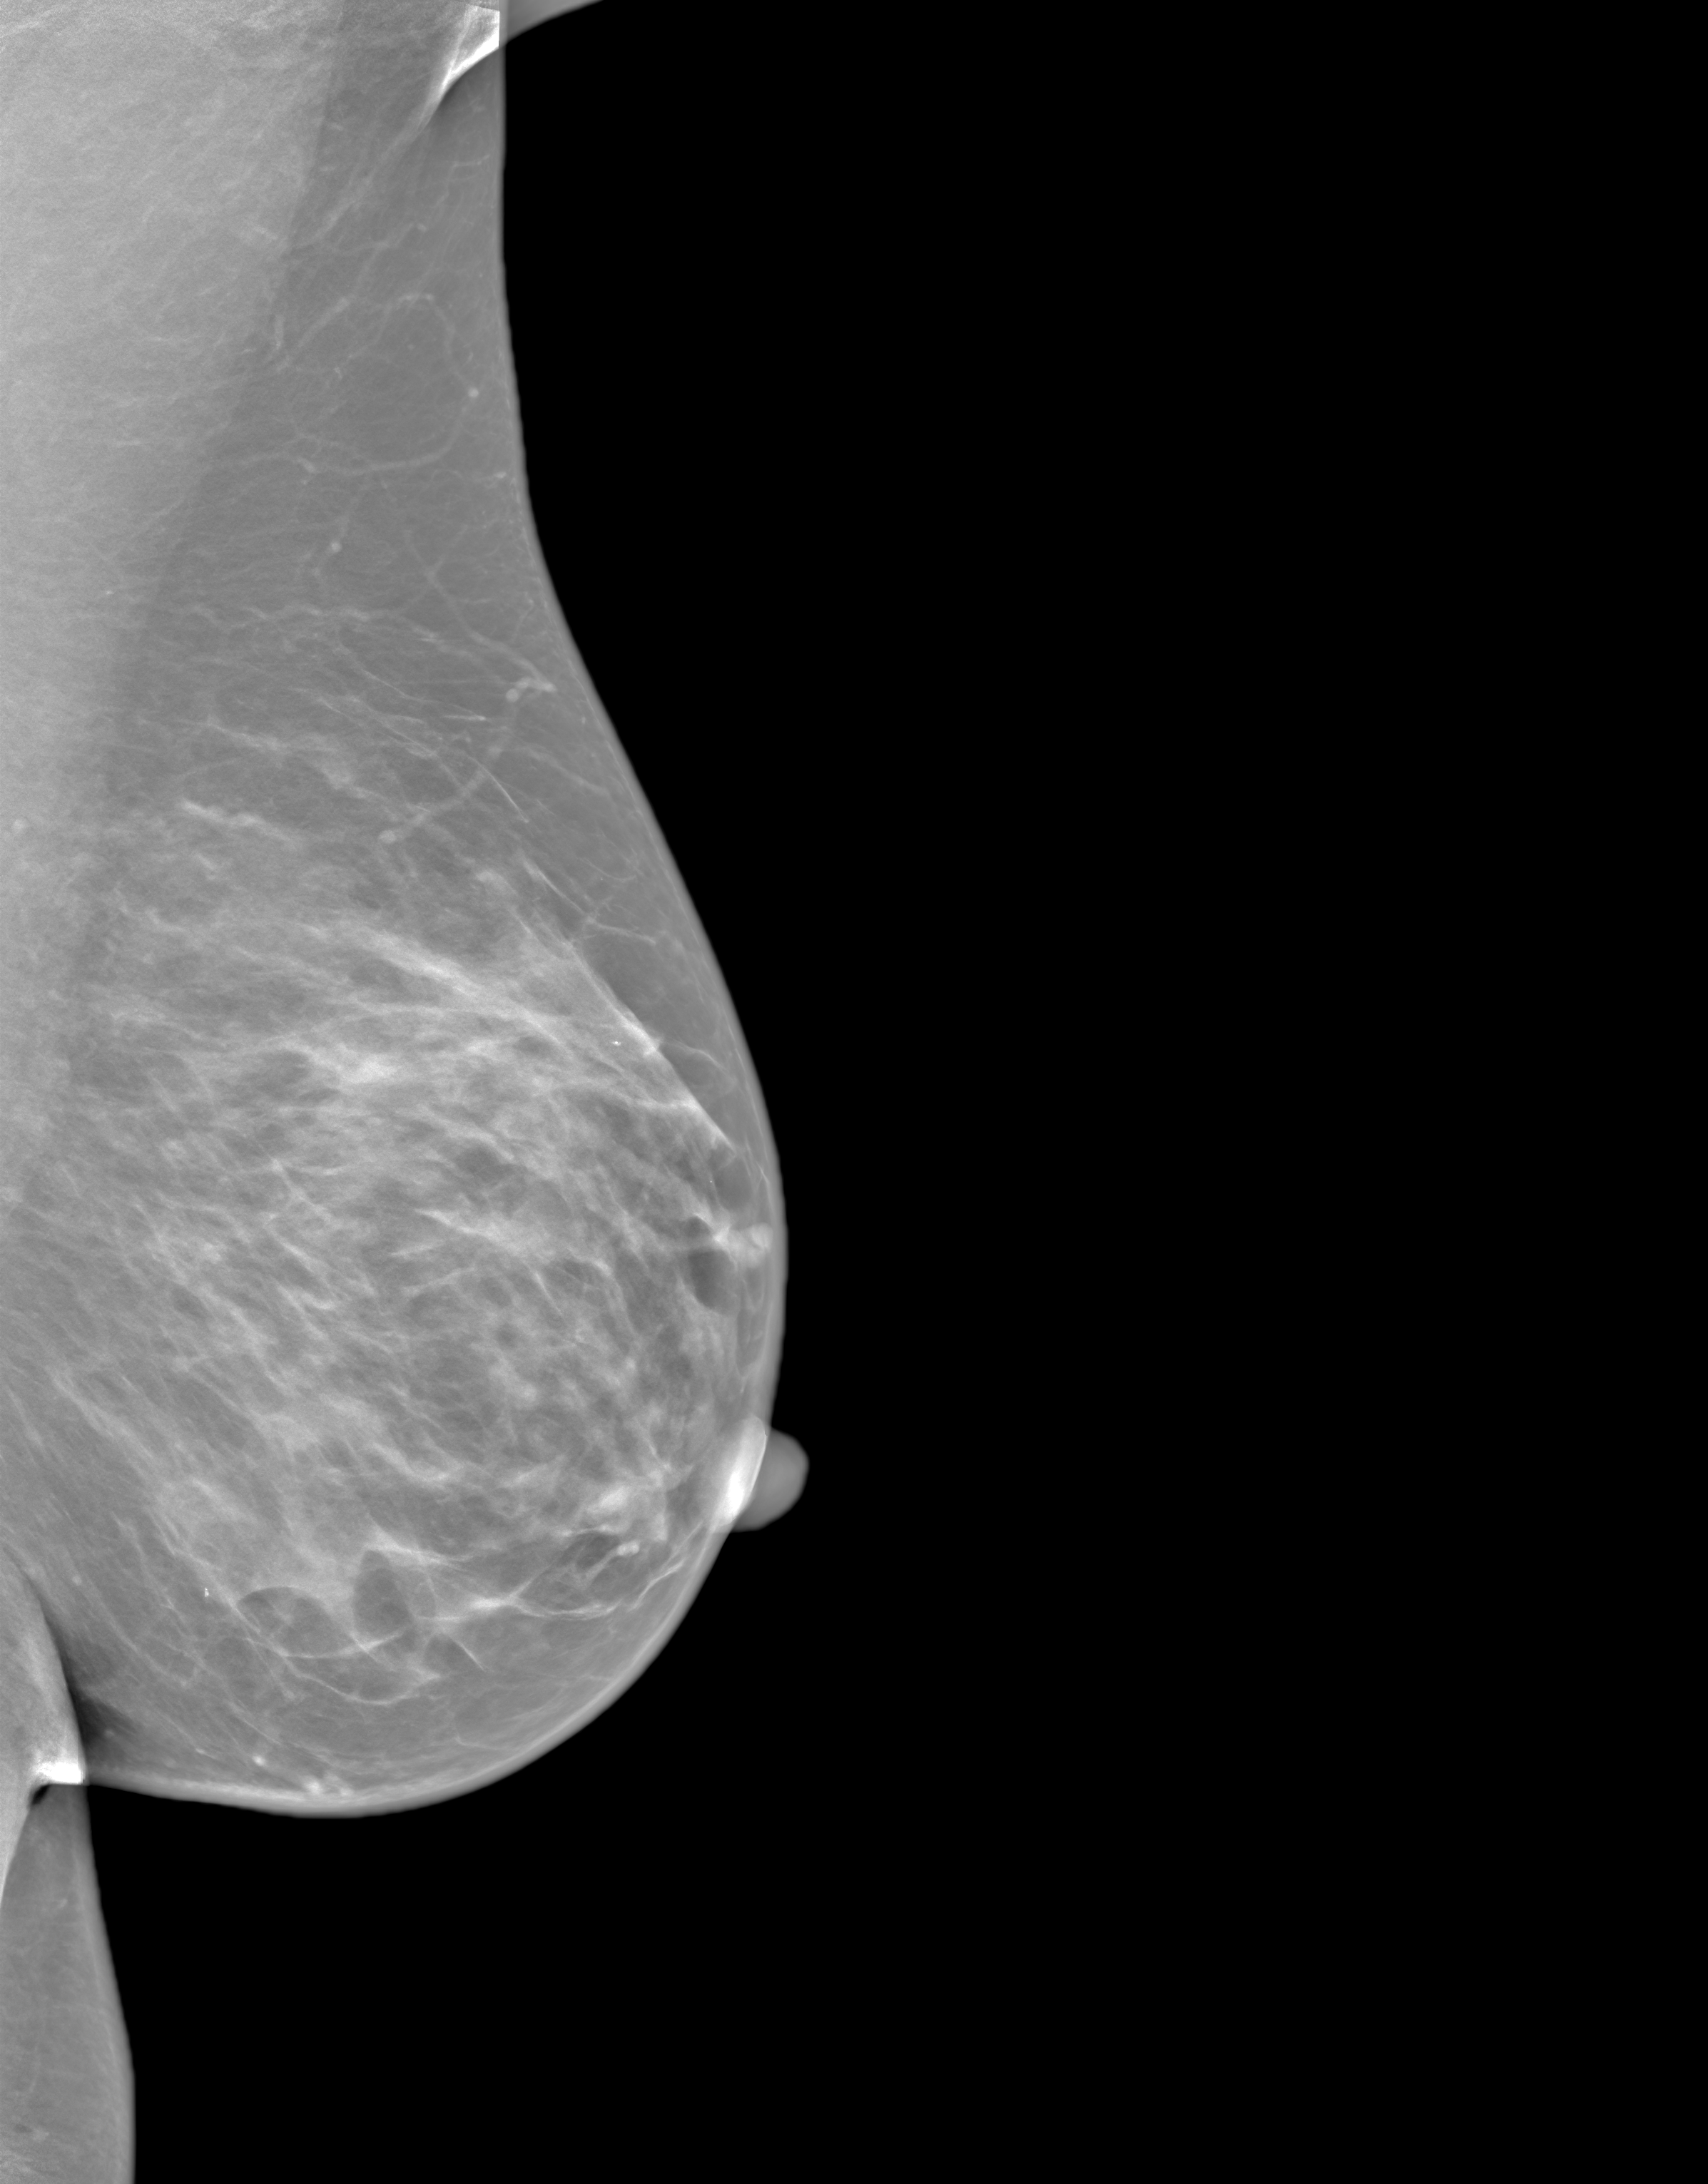
Screening examination. Female patient, age 50 years.
Image type: synthesized 2-D view from tomosynthesis. Breast: left. Projection: MLO view.